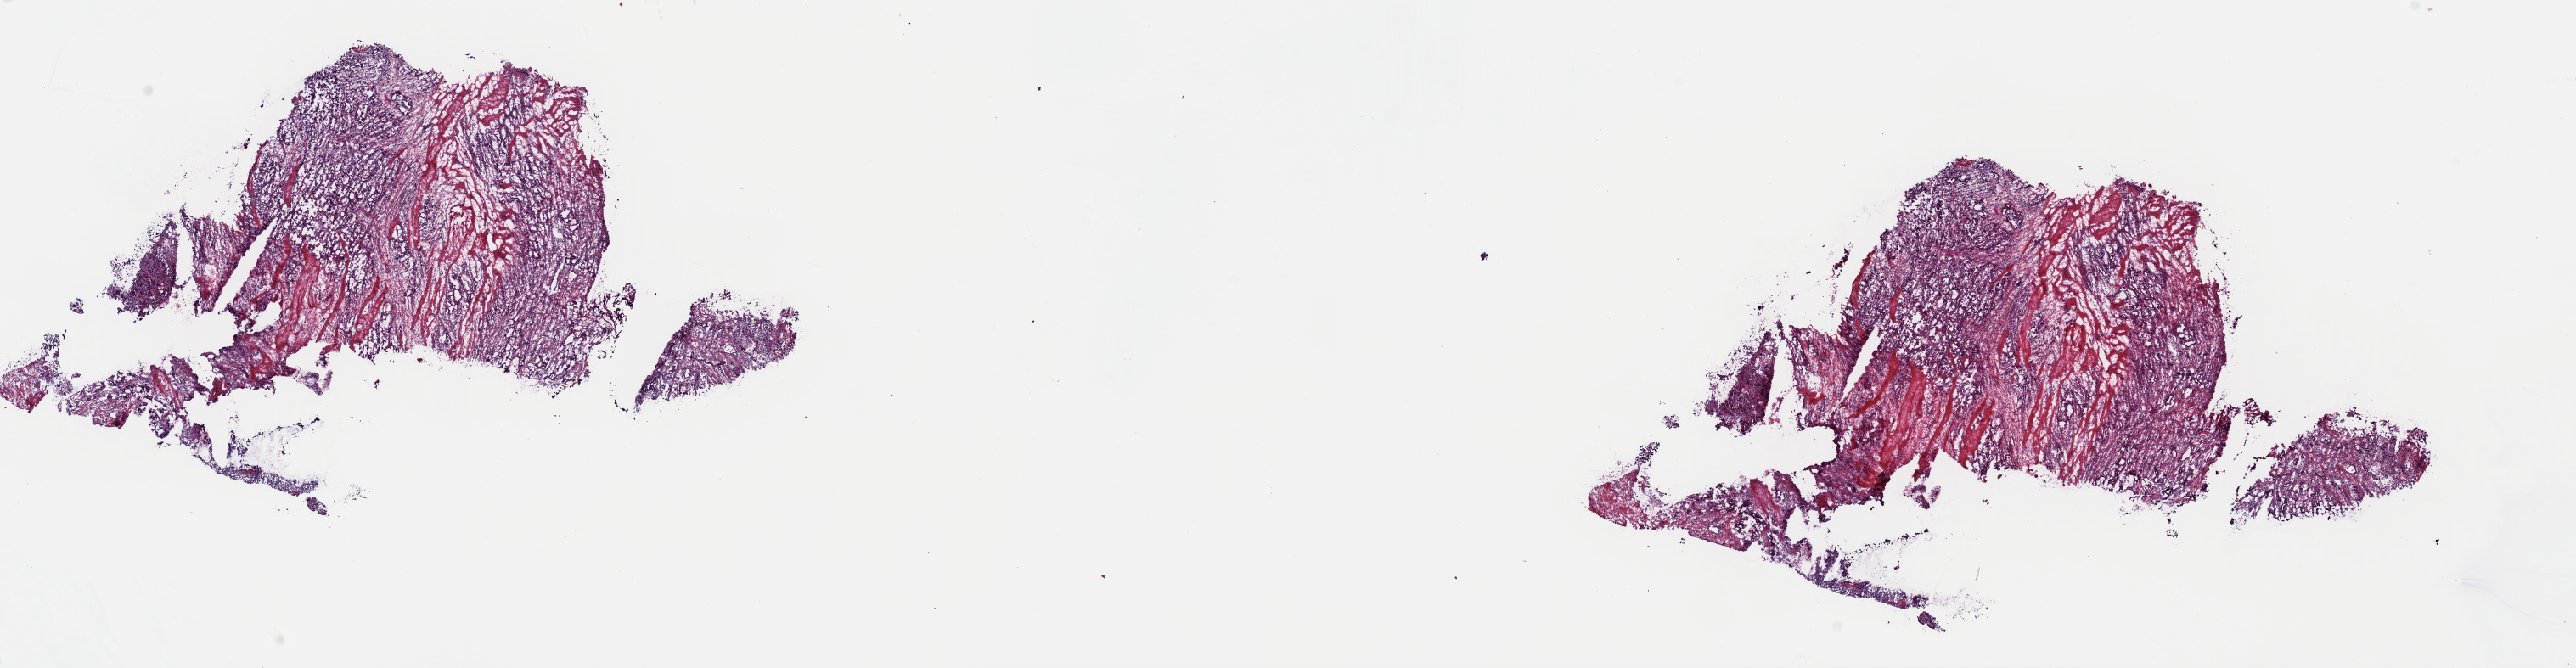
Digitized Hematoxylin and eosin (H&E) stained tissue section (whole slide) — whole scanned area (about 24.0 x 6.2 mm, from a 40x scan) shown as a low-resolution overview; frozen section from the top of the tissue portion; stomach, primary tumour sample. Male patient; age at initial diagnosis 62 years. Histologic grade: G1 (well differentiated). Slide review estimates, as recorded: tumour cells 60%, tumour nuclei 70%, normal cells 0%, stromal cells 40%, necrosis 0%. Inflammatory infiltration, as recorded: lymphocyte infiltration 0%, monocyte infiltration 0%, neutrophil infiltration 0%.
Diagnosis: Adenocarcinoma, NOS (gastric antrum). AJCC pathologic stage: IIIA.